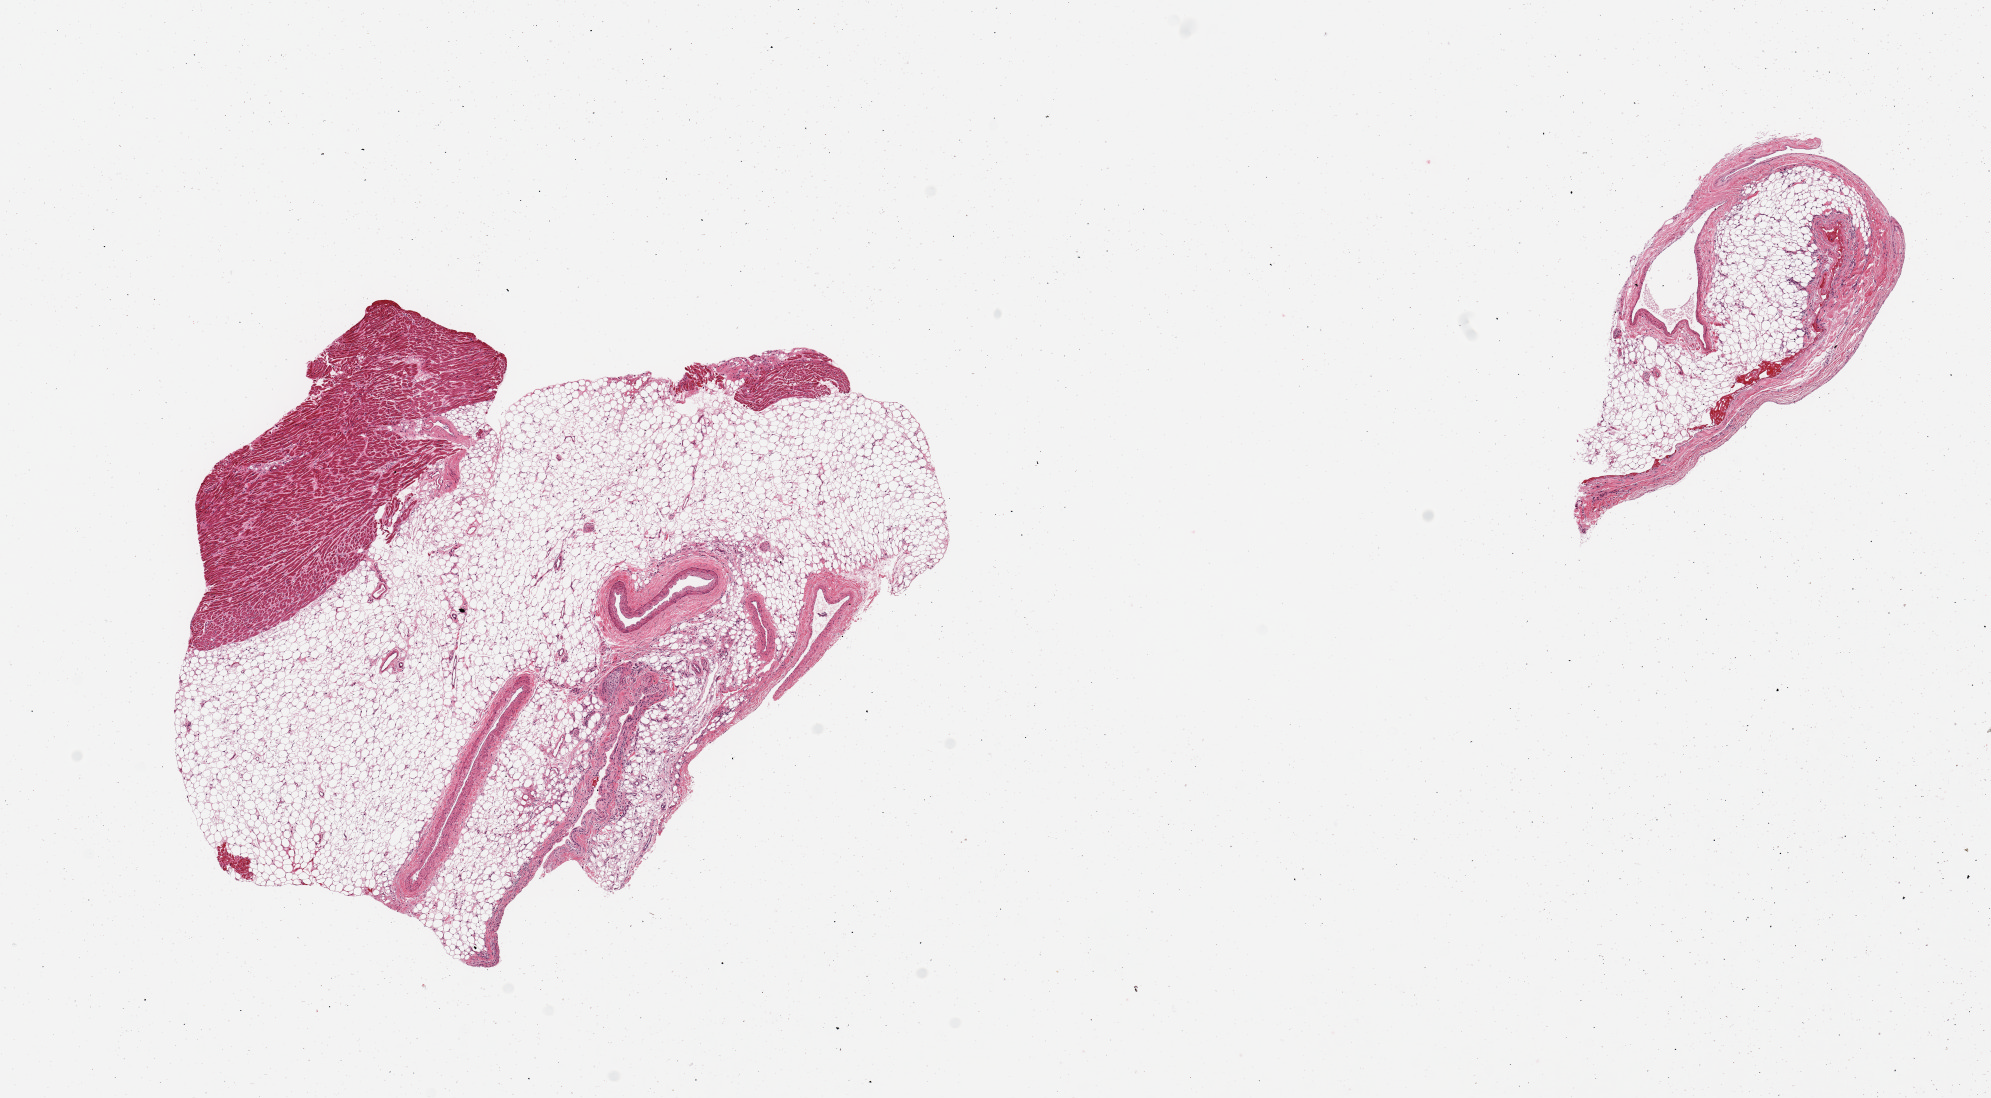
Digitized hematoxylin and eosin (H&E)-stained section, shown as a low-resolution overview of the whole scanned area (about 15.8 x 8.7 mm, acquisition: 20x scan); PAXgene-fixed paraffin-embedded (PFPE) section; target tissue: coronary artery; tissue donor sample. Male donor.
Pathologist's review note for this sample: 2 pieces; inadequate samples: 80% fat and myocardium; small arteries and veins.